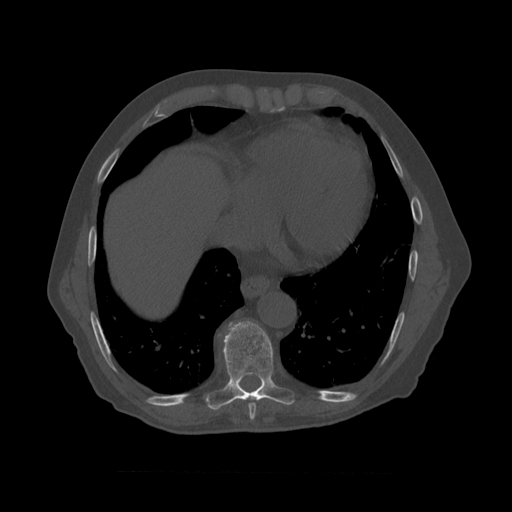
CT including the spine, one axial slice; slice 448 of 450 in the series (ordered by position); 120 kVp; bone window (W 1800 / L 400 HU); 512 × 512 image matrix, field of view 405 × 405 mm. Patient age 75 years. From the clinical record (not read from this slice): primary cancer: prostate.
Annotated regions visible in this slice (semi-automatic segmentation, software-assisted and operator-edited):
- T8 vertebra: box from (x=218, y=321) to (x=295, y=411) px